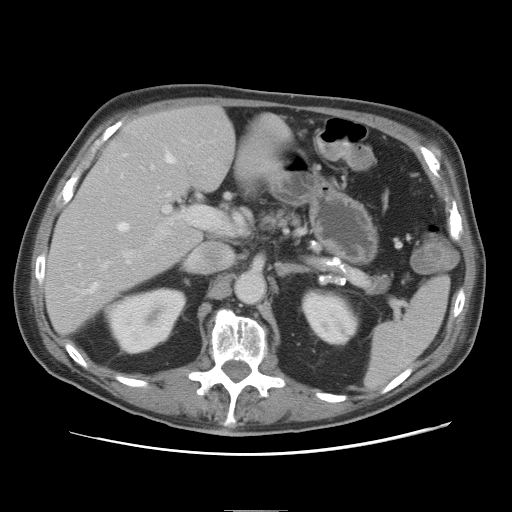
Contrast-enhanced abdominal CT, one axial slice; position 43 of 89 along the scan axis; intravenous contrast given; soft-tissue window (W 400 / L 40 HU); 5 mm slice thickness; 512 × 512 image matrix. Male patient, age 69 years. From the clinical record (not read from this slice): diagnosis: colorectal cancer liver metastases, imaged before liver resection; multiple liver metastases: no; largest metastasis: 8.5 cm; disease in both lobes: no.
Outlined on this slice (manually delineated by an expert):
- hepatic veins: bounding box [x1, y1, x2, y2] px = [85, 152, 176, 293]
- liver: [43, 107, 289, 332]
- planned liver remnant (the part of the liver to remain after resection): [42, 107, 235, 331]
- portal vein (with intrahepatic branches): [104, 165, 223, 267]